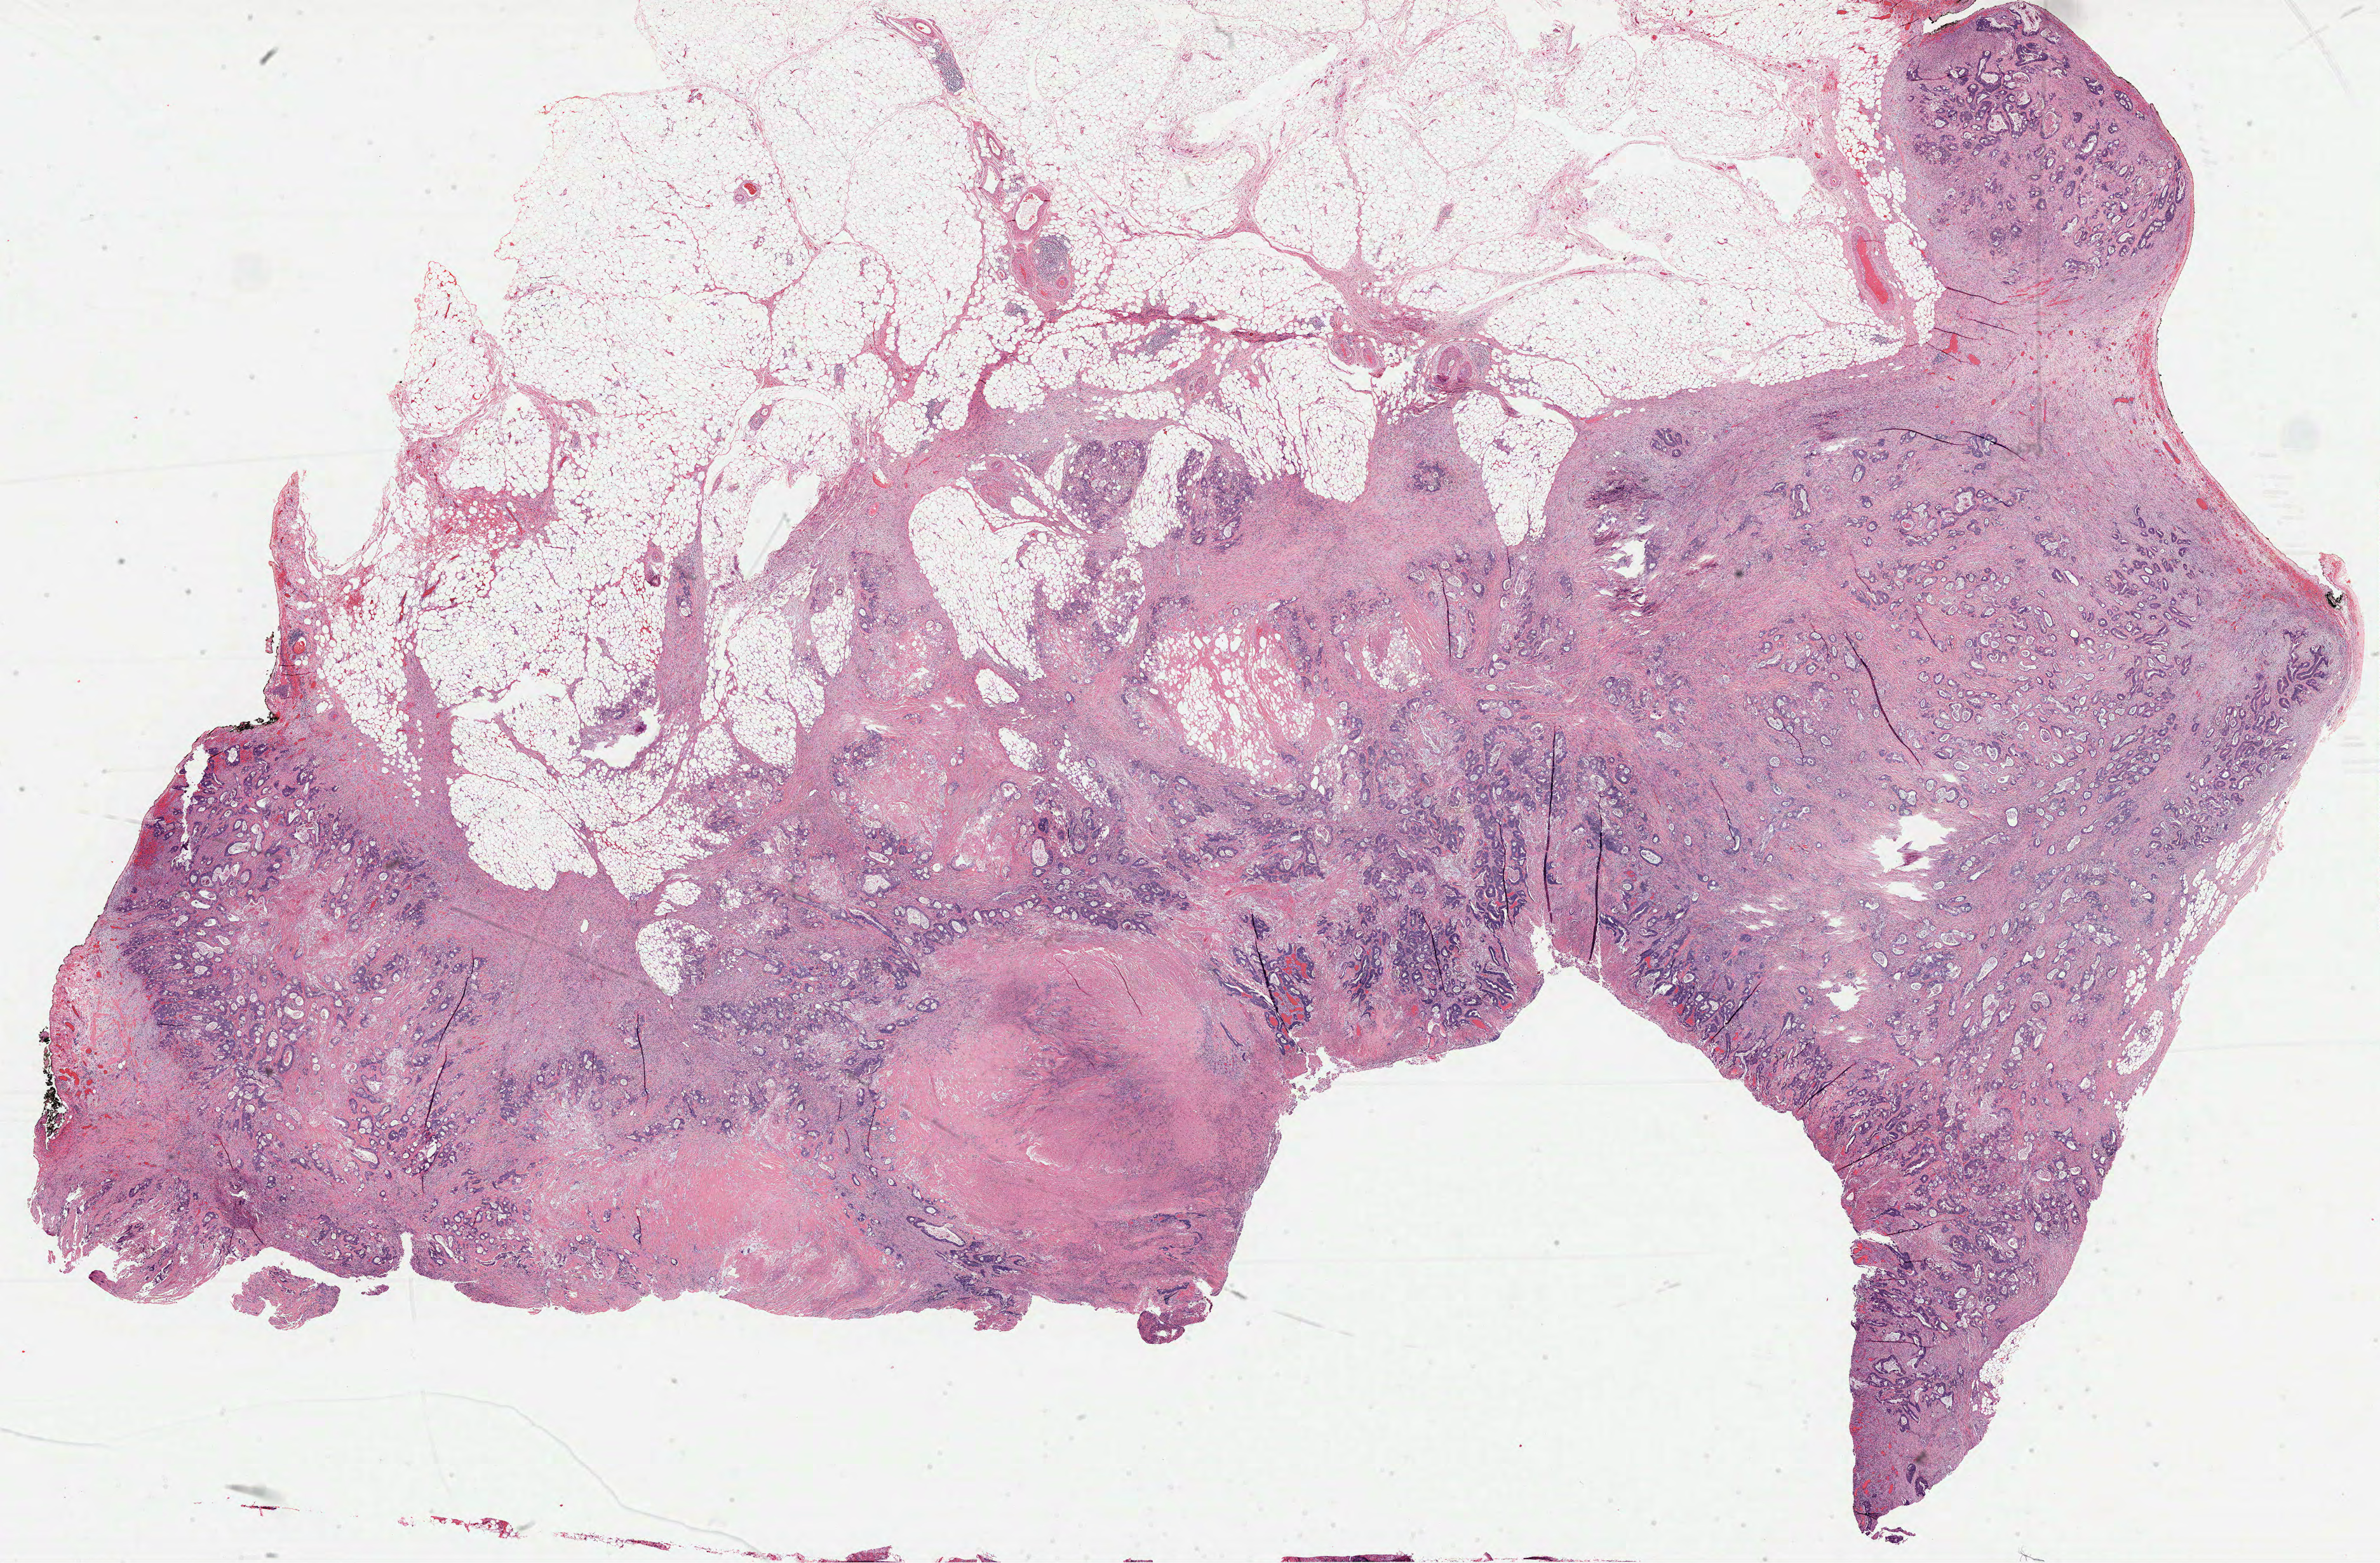
Digitized Hematoxylin and eosin (H&E) stained tissue section (whole slide) — a low-resolution overview of the entire scanned area, about 30.2 x 19.8 mm (slide scanned at 40x). Formalin-fixed paraffin-embedded (FFPE) diagnostic section. Primary tumour sample from the colon. Female patient; age at initial diagnosis 46 years.
AJCC pathologic stage: IIIB. Lymph nodes positive (case pathology): 3 of 12 examined. Pathologic diagnosis: Adenocarcinoma, NOS.